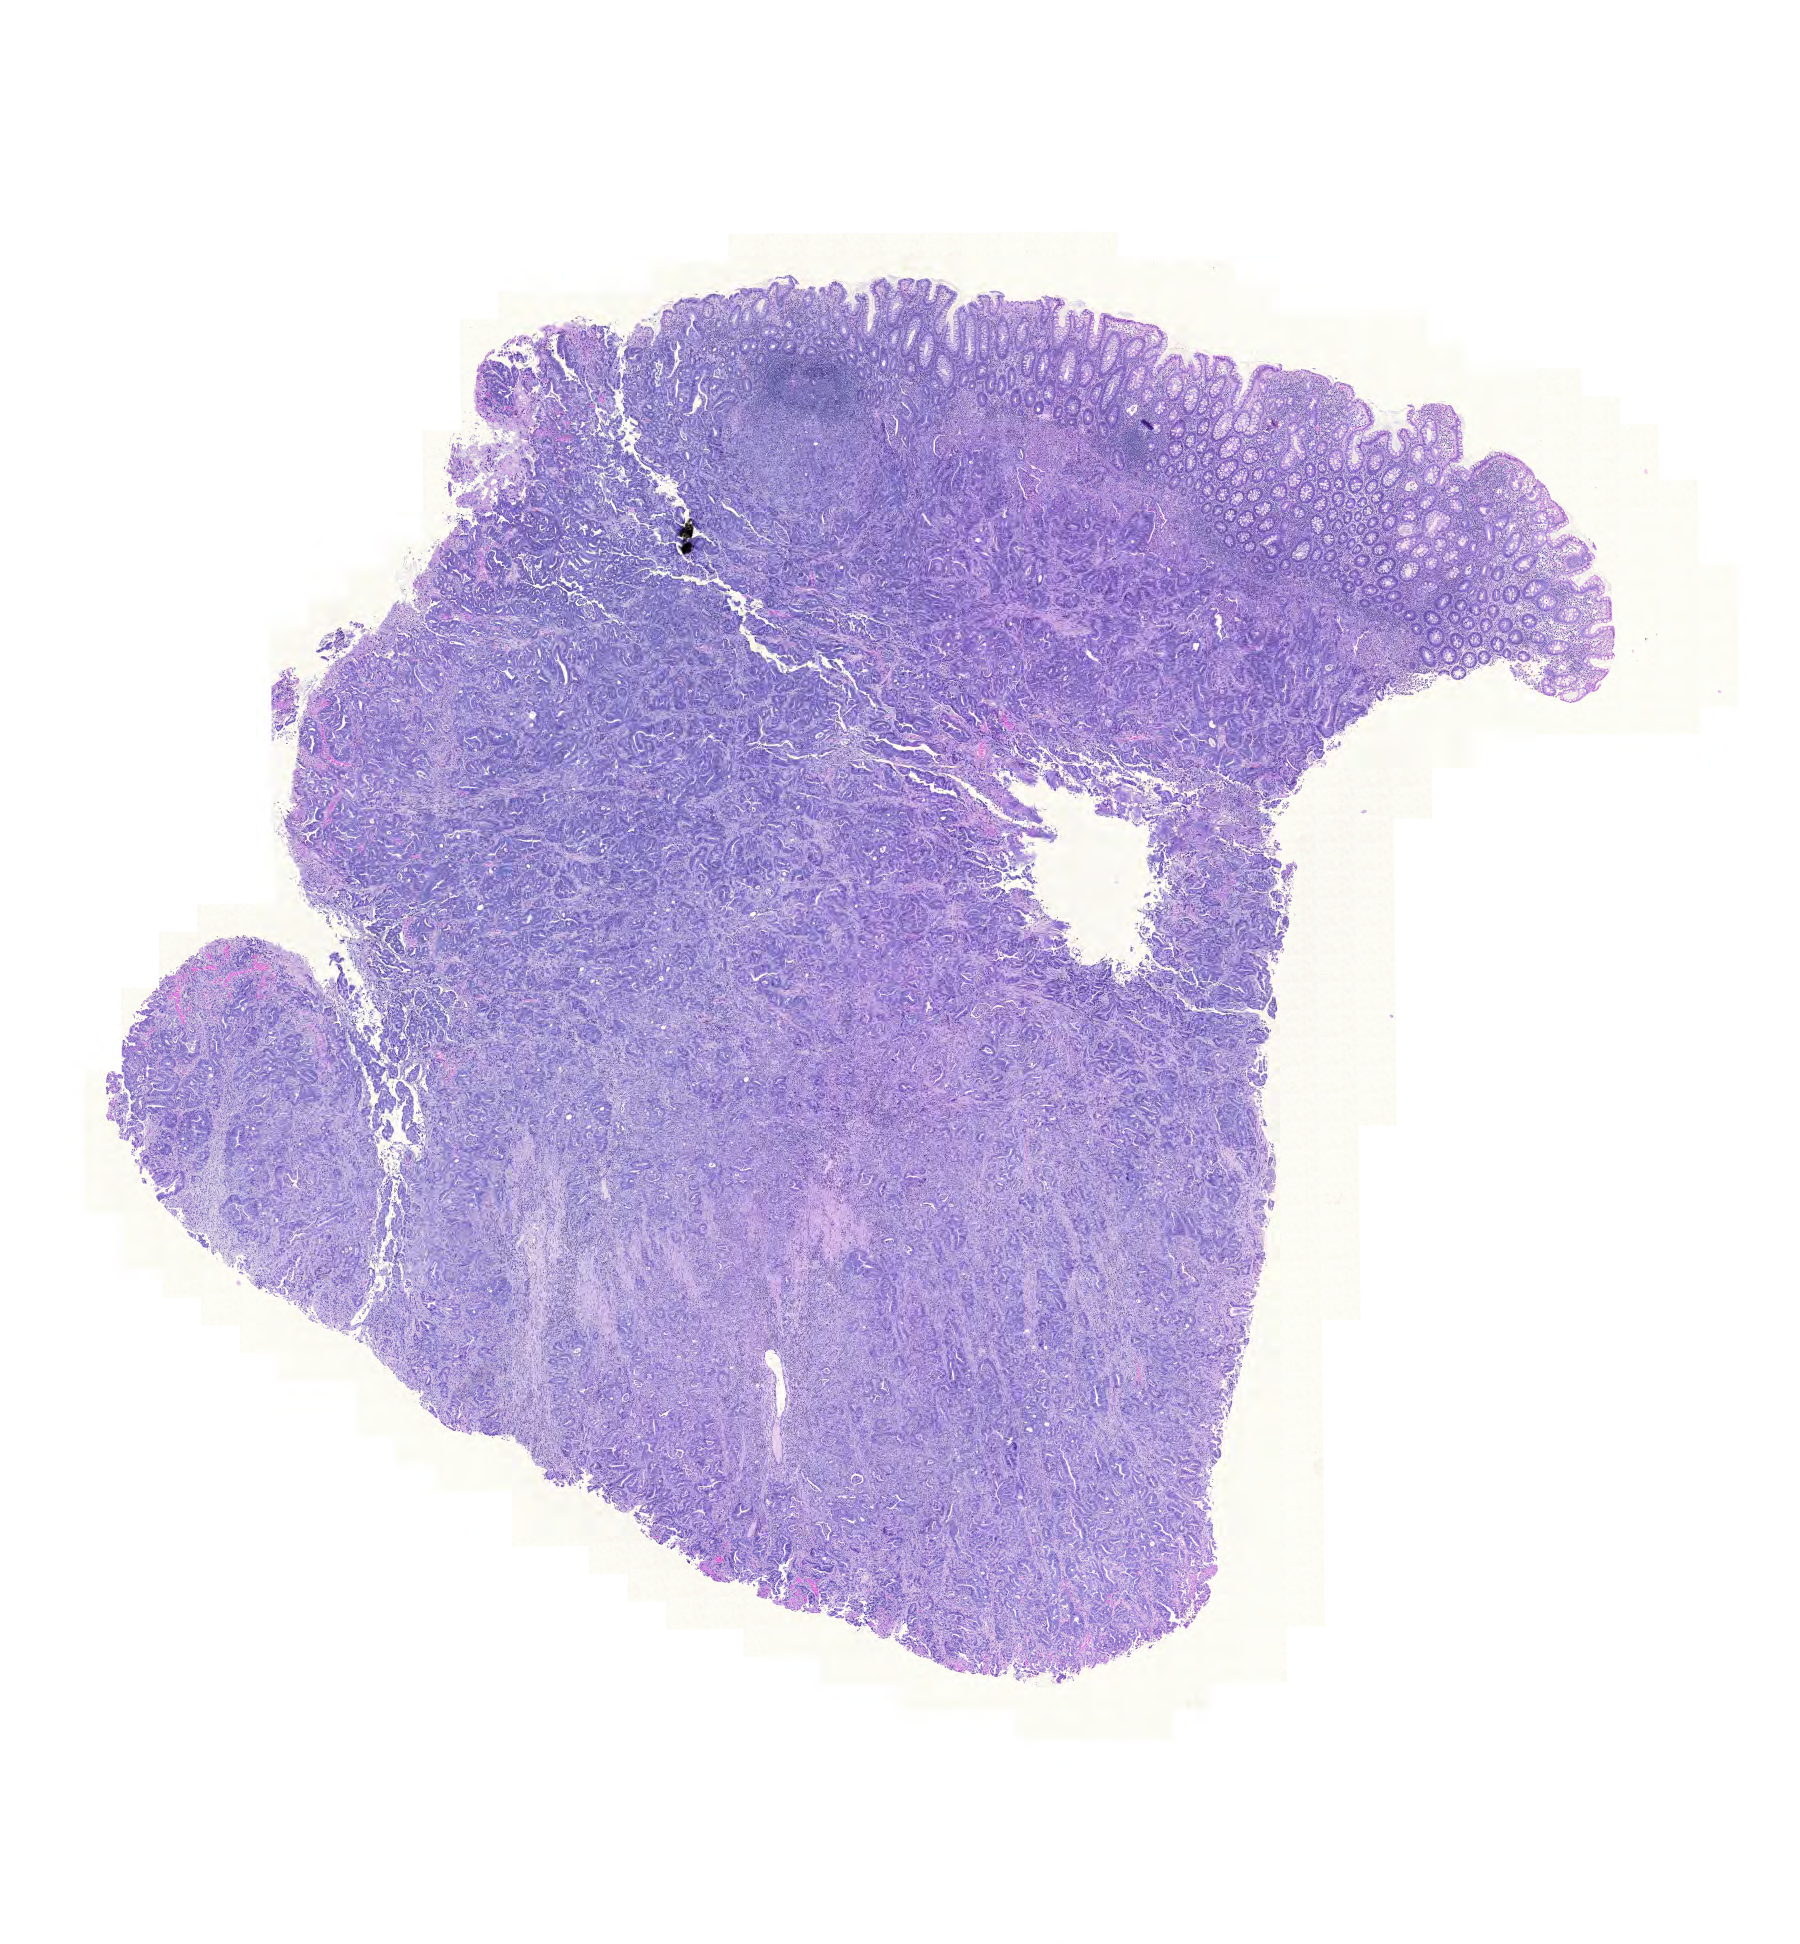
Whole-slide histology image, H&E, low-resolution overview of the scanned area, about 13.4 x 14.5 mm (acquisition: 20x scan); formalin-fixed paraffin-embedded (FFPE) diagnostic section; primary tumour sample from the colon. Patient: female, age at initial diagnosis 62 years.
Histologic diagnosis: Adenocarcinoma, NOS (ascending colon). Lymph nodes positive (case pathology): 0 of 39 examined. AJCC pathologic stage: IIA (6th edition). TNM: T3 N0 M0.